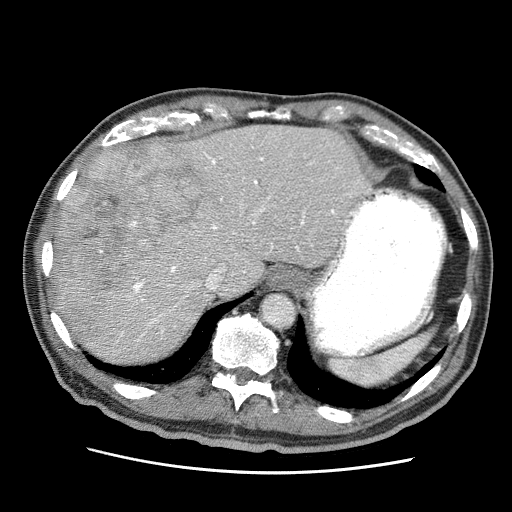
Contrast-enhanced abdominal CT (liver protocol), one axial slice; position 49 of 75 along the scan axis; soft-tissue window (W 400 / L 40 HU); 512 × 512 image matrix, field of view 360 × 360 mm. From the clinical record (not read from this slice): diagnosis: hepatocellular carcinoma (patient treated with transarterial chemoembolisation; whether this scan precedes or follows treatment is not stated here); TNM stage (as recorded): Stage-IIIA.
Outlined on this slice (semi-automatic segmentation, software-assisted and operator-edited):
- abdominal aorta: bounding box [x1, y1, x2, y2] px = [262, 294, 295, 328]
- liver parenchyma outside the tumour (the mass and vessels are separate outlines, so this box may not span the whole liver): [54, 124, 371, 362]
- mass: [59, 146, 214, 346]
- liver vessels: [120, 146, 351, 341]